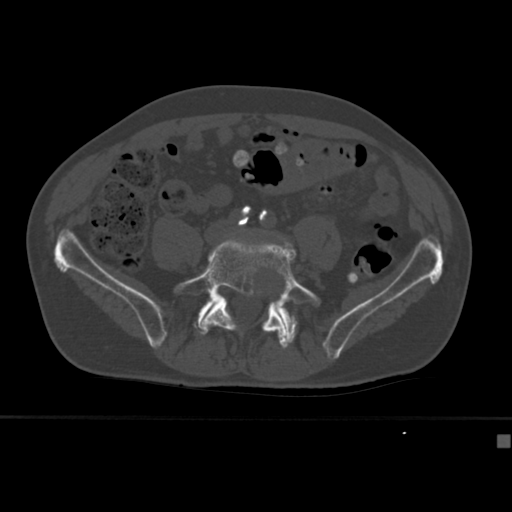
CT including the spine, one axial slice. Slice 86 of 430 in the series (ordered by position). 120 kVp. Bone window (W 1800 / L 400 HU). 1.5 mm slice thickness. 512 × 512 image matrix, field of view 337 × 337 mm. Patient: male, 64 years. From the clinical record (not read from this slice): primary cancer: uterus; vertebrae with lytic lesions (as recorded): T1, T4, T5, T7, L5.
Annotated regions visible in this slice (semi-automatic segmentation, software-assisted and operator-edited):
- L5 vertebra: bounding box <174,237,321,349> (left, top, right, bottom; pixels)